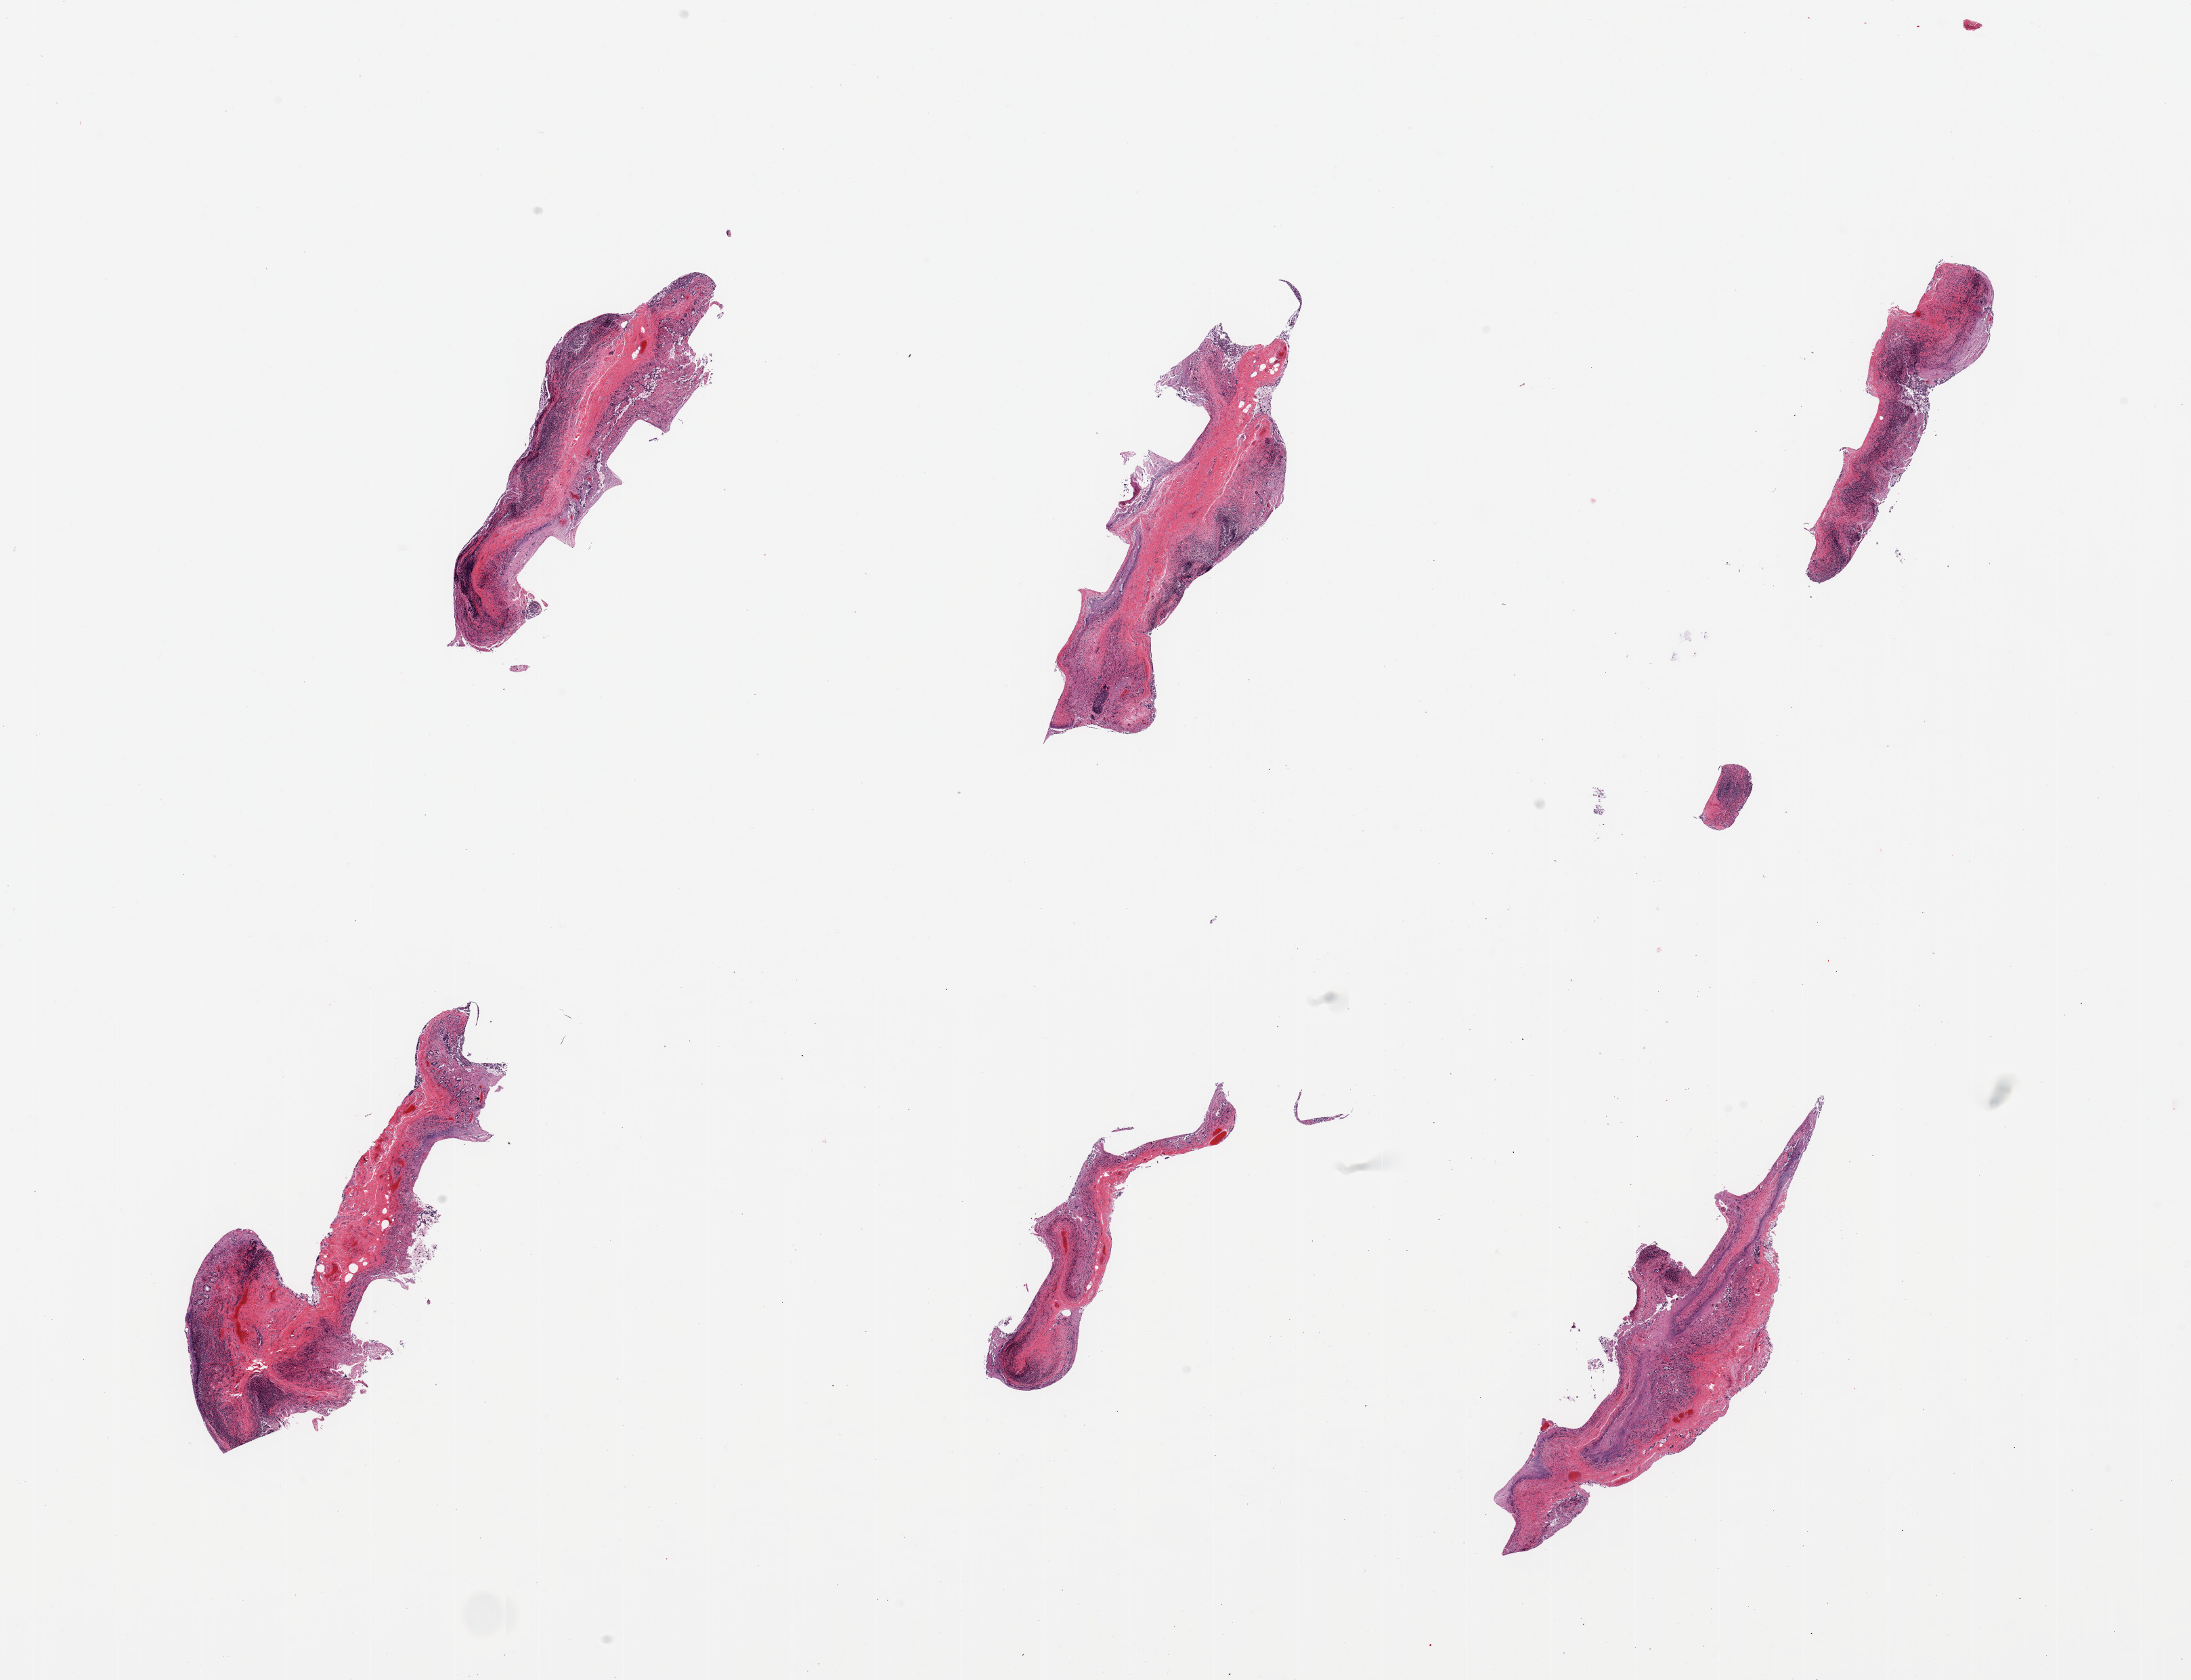
Digitized hematoxylin and eosin (H&E)-stained section, low-resolution overview of the scanned area, about 25.6 x 19.6 mm, PAXgene-fixed paraffin-embedded (PFPE) section, target tissue: ileum, tissue donor sample. Donor sex: male.
Review note (as recorded): 6 pieces; abundant lymphoid tissue in several pieces; mucosa autolyzed.